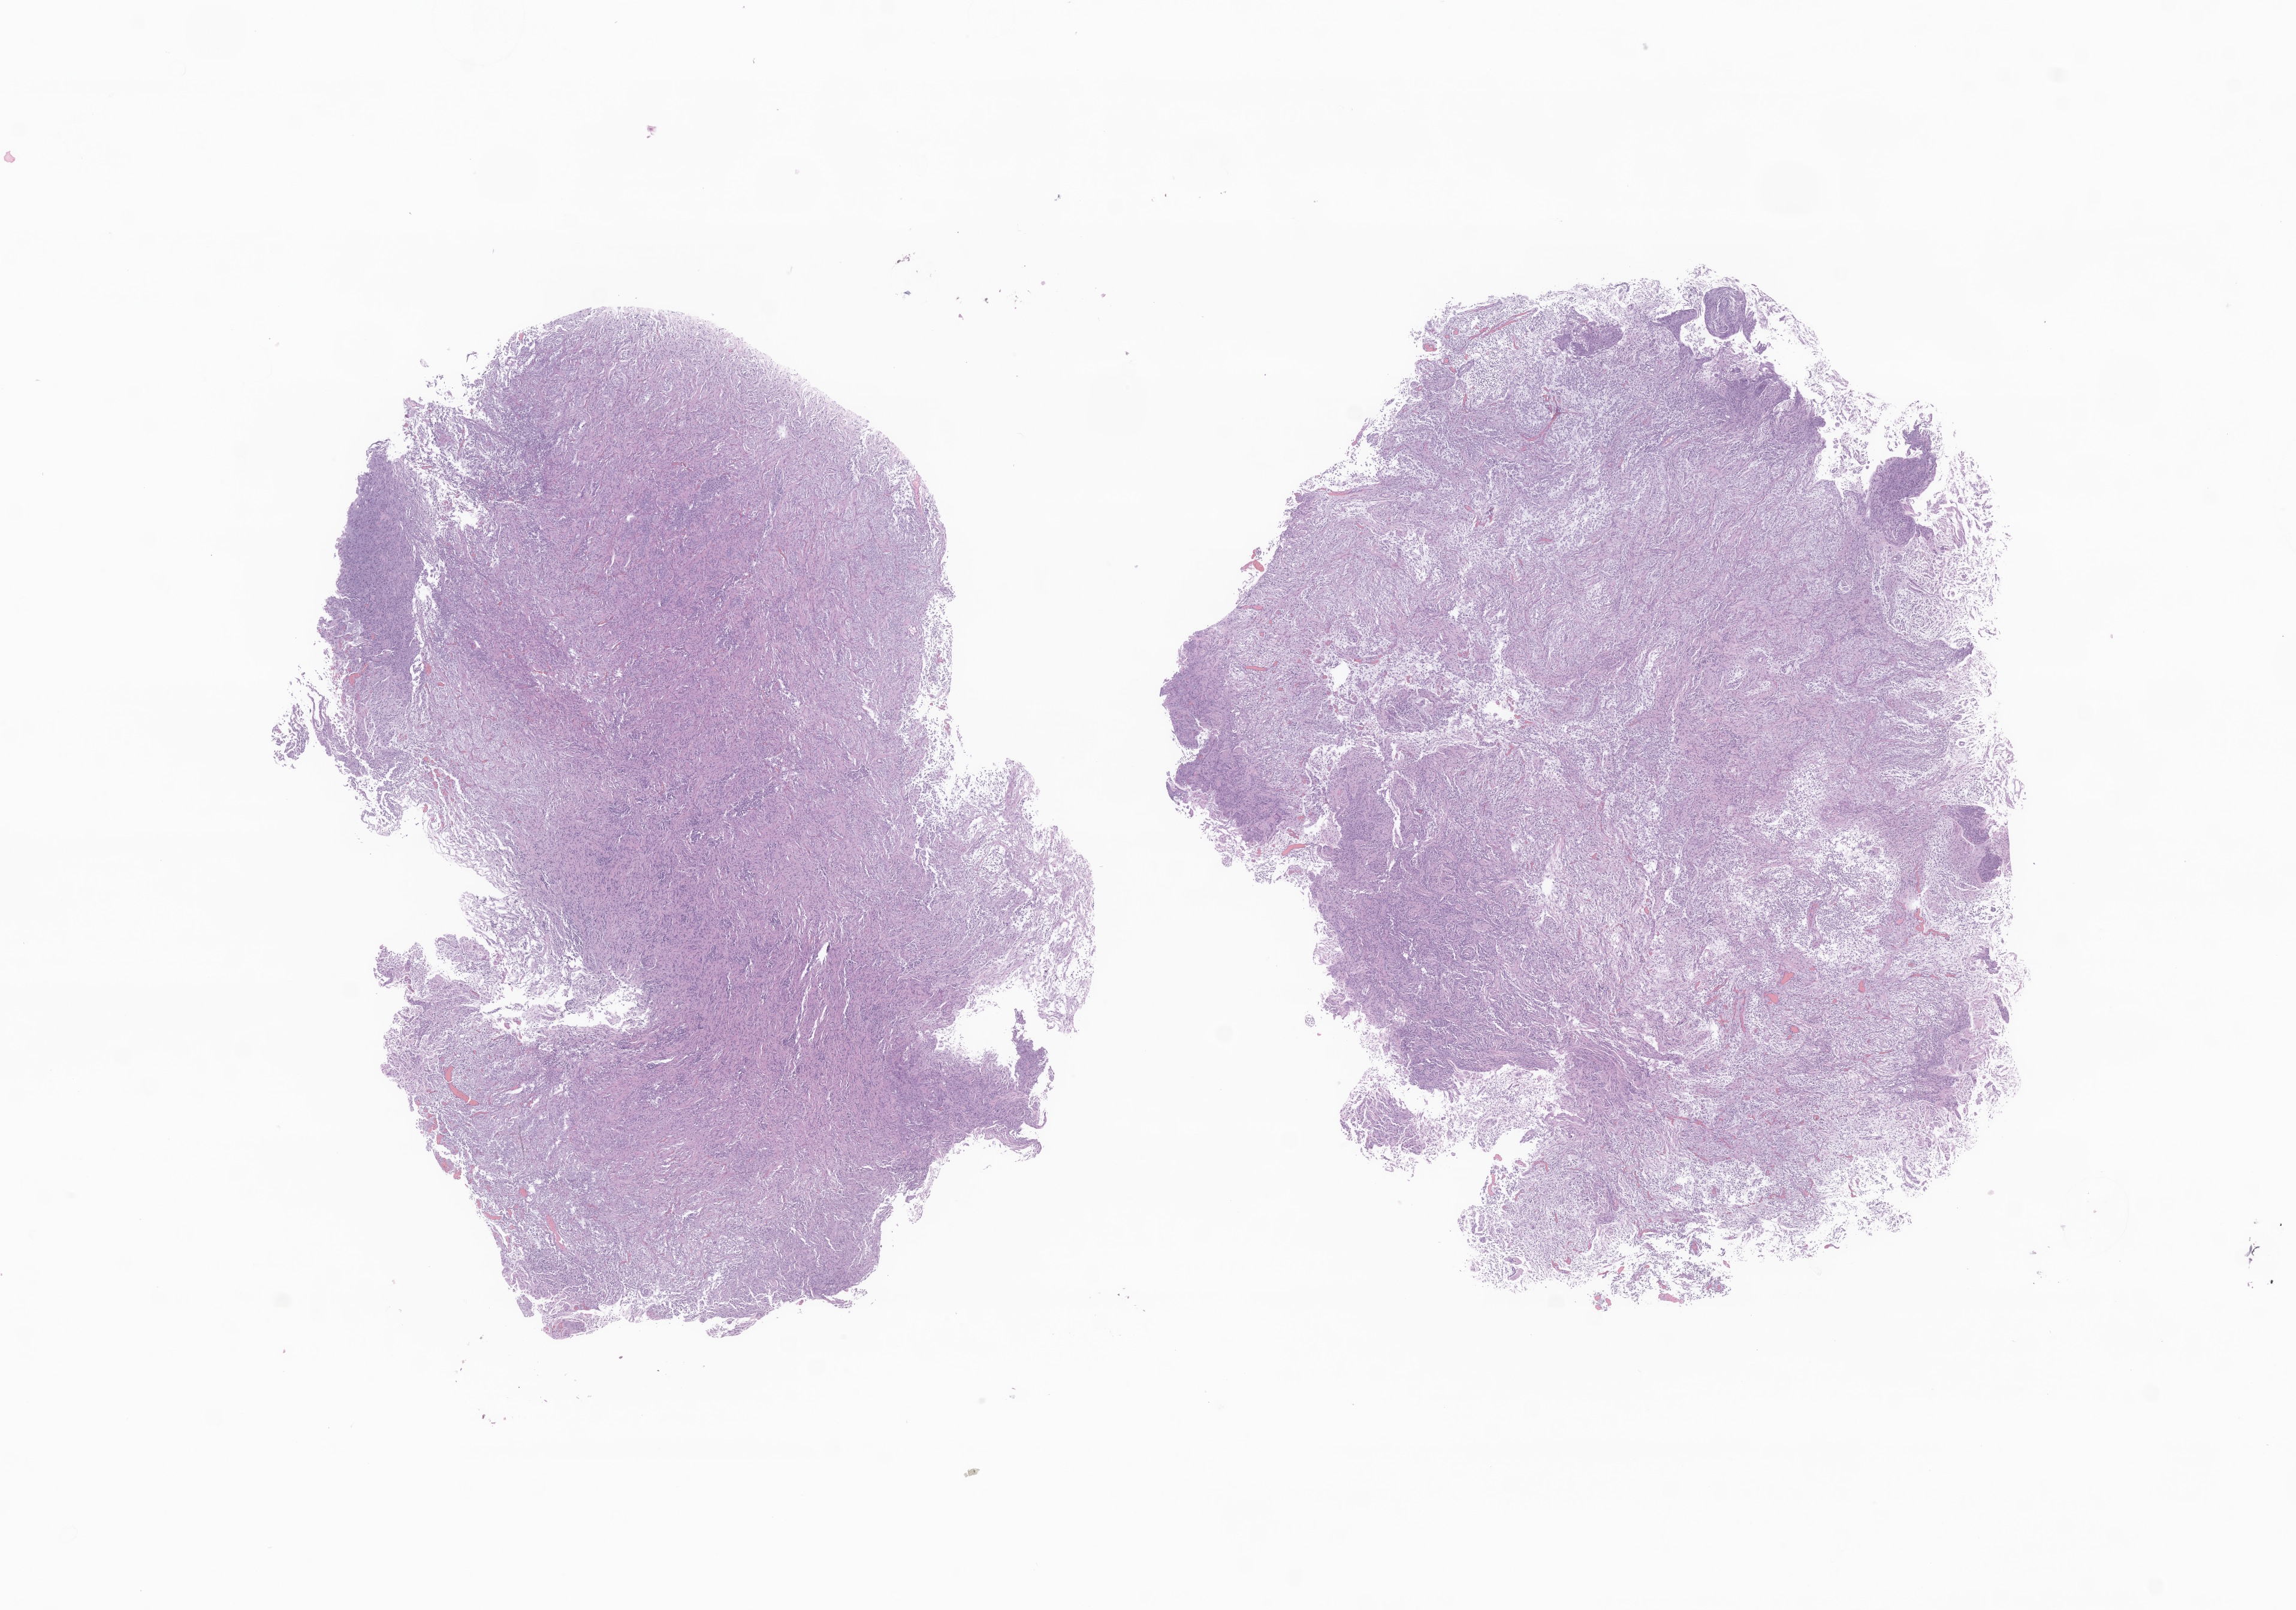
Hematoxylin and eosin (H&E) whole-slide image of tumor tissue from the brain, low-resolution overview of the scanned area, about 16.2 x 11.3 mm, formalin-fixed, paraffin-embedded (FFPE) tissue. Patient: female, age 141 days.
Diagnosis: Glioma, malignant.